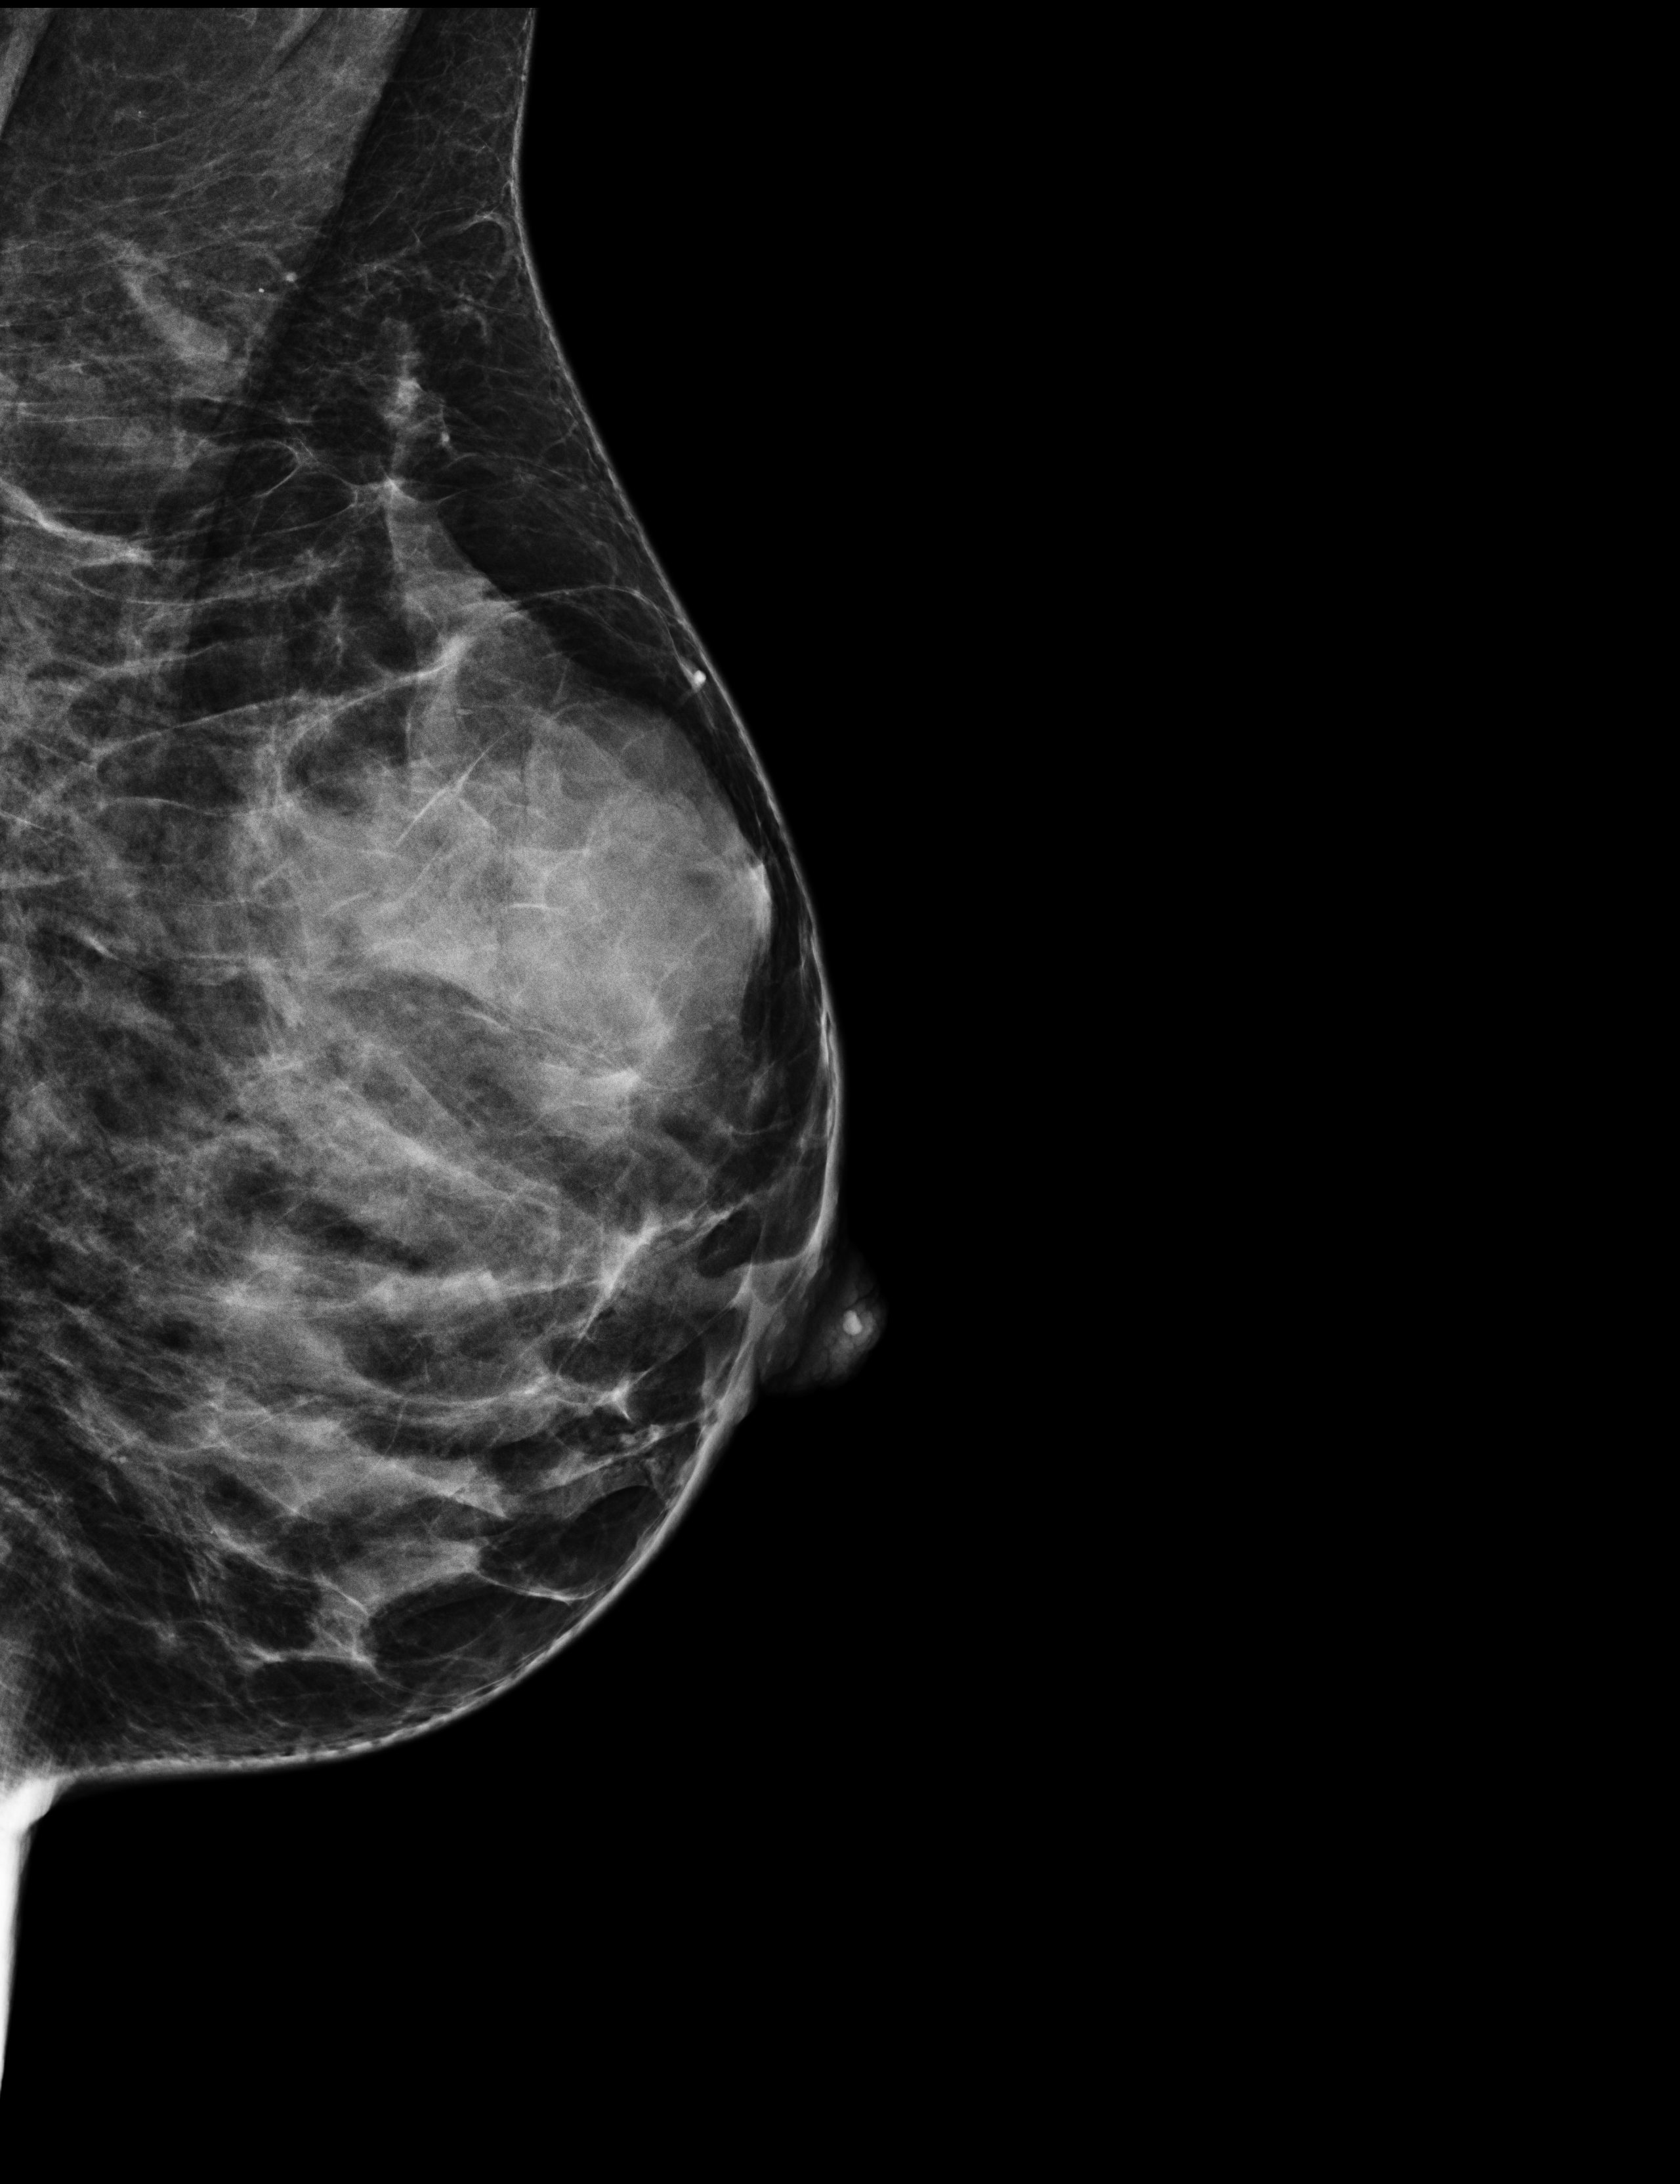
Digital mammogram (FFDM); left breast; mediolateral oblique (MLO) view; screening examination. Female patient, age 49 years.
- BI-RADS breast density category at the screening exam (both breasts, scale 1–4): 3
- final BI-RADS category for the screening round (tomosynthesis exam, both breasts): category 1
- recall: no recall after this screen